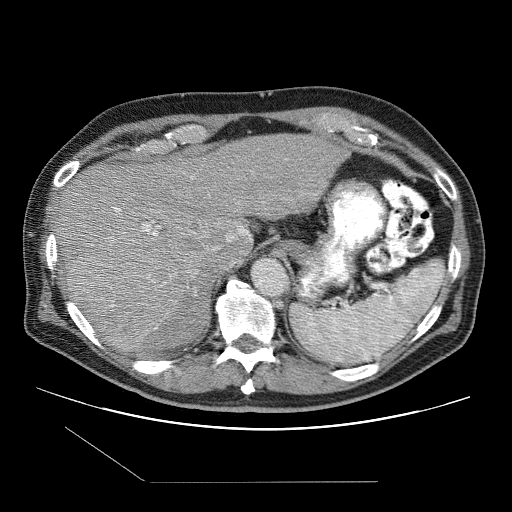
Contrast-enhanced abdominal CT (liver protocol), one axial slice; position 75 of 109 along the scan axis; reconstruction kernel STANDARD; one of 2 acquisitions stored at this slice position; soft-tissue window (W 400 / L 40 HU); 512 × 512 image matrix, field of view 400 × 400 mm. Case-level facts recorded for this patient, not image findings: diagnosis: hepatocellular carcinoma (patient treated with transarterial chemoembolisation; whether this scan precedes or follows treatment is not stated here); TNM stage (as recorded): Stage-IIIB; Child-Pugh class: A; tumour nodularity: multinodular.
Structures marked on this image (semi-automatically segmented with operator editing):
- liver parenchyma outside the tumour (the mass and vessels are separate outlines, so this box may not span the whole liver): bounding box (x1, y1, x2, y2) in pixels: (56, 134, 346, 352)
- mass: (68, 246, 198, 351)
- liver vessels: (114, 177, 249, 249)